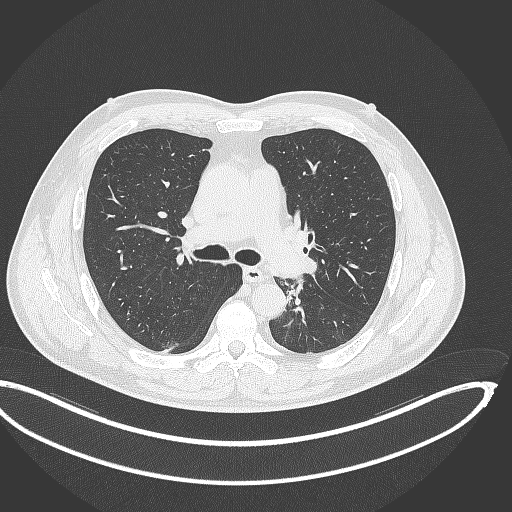
Chest CT, one axial slice. Slice 223 of 362 in the series (ordered by position). Lung window (W 1500 / L -600 HU). 1 mm slice thickness. 512 × 512 image matrix, field of view 442 × 442 mm. Patient: male, 50 years. Case-level facts recorded for this patient, not image findings: clinical TNM (as recorded): T2a N3 M0.
Outlined on this slice (bounding box drawn by a radiologist):
- lung tumour (recorded histology: squamous cell carcinoma): box from (x=292, y=275) to (x=309, y=289) px